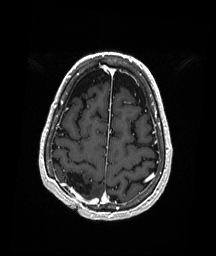
Brain MRI from a brain-tumour surgery series, one axial slice. Position 56 of 192 along the scan axis. T1-weighted post-contrast. 1 mm slice thickness. 216 × 256 image matrix. Case-level facts recorded for this patient, not image findings: histopathology: Astrocytoma; WHO grade: 3; IDH mutation: yes; tumour location: Right Parietal.
Annotated regions visible in this slice (expert manual segmentation):
- previous resection cavity: box from (x=62, y=171) to (x=93, y=196) px